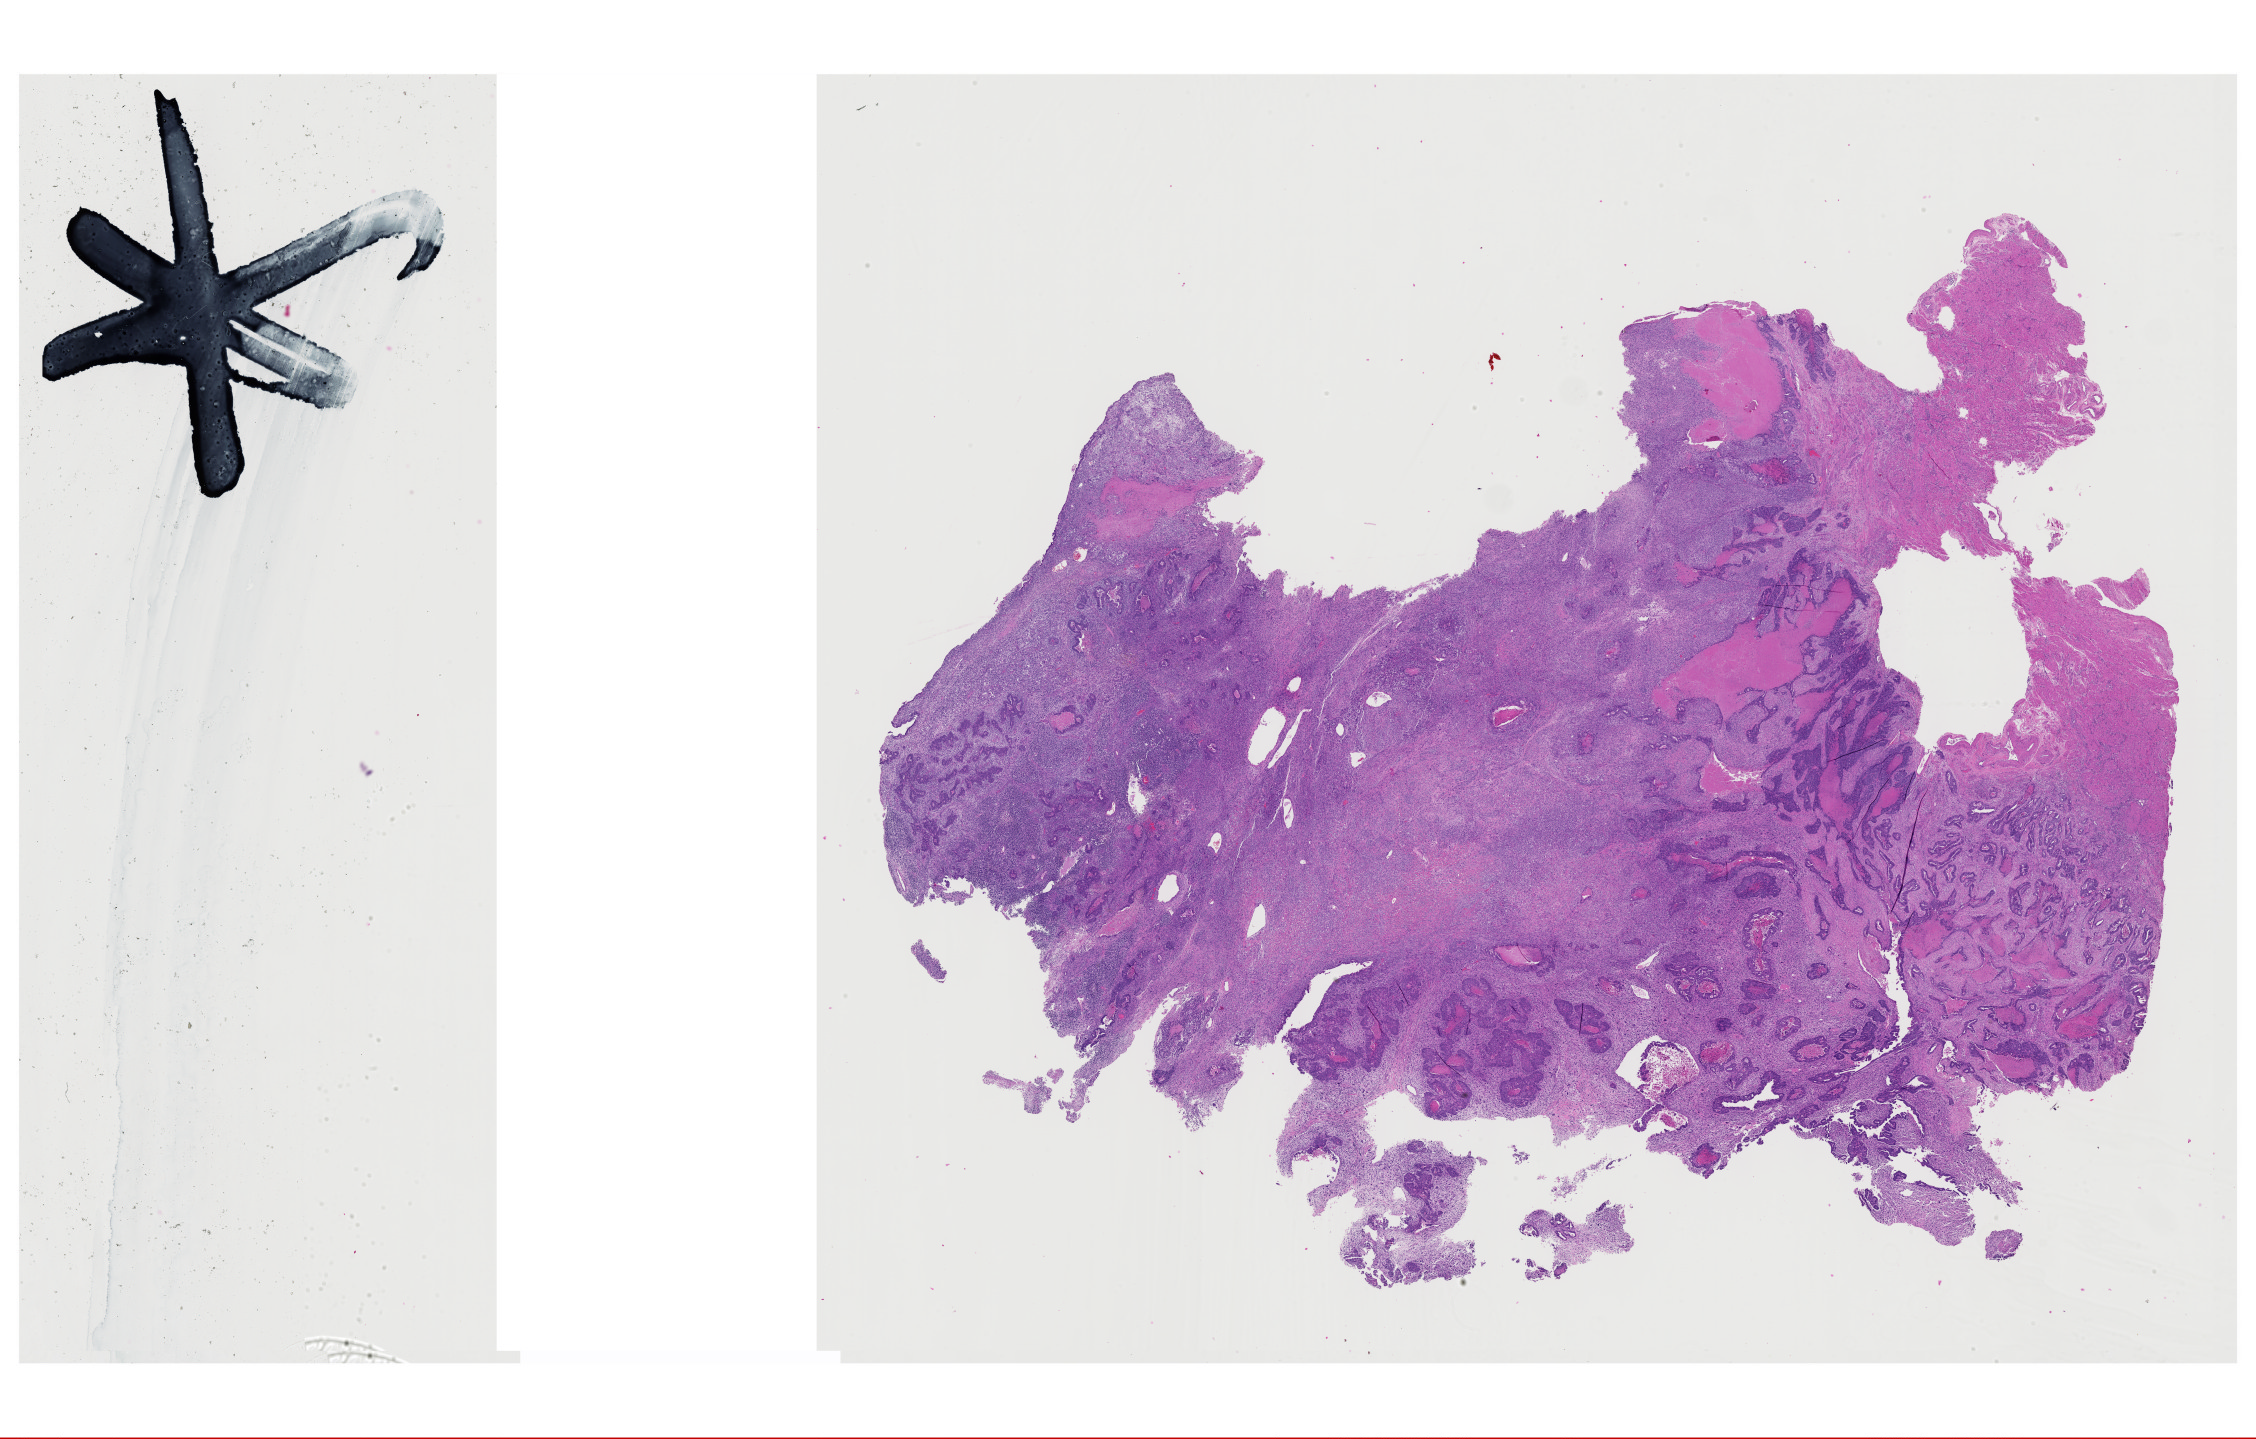
H&E whole-slide image — low-resolution overview of the scanned area, about 36.1 x 23.0 mm; FFPE section; sample: primary tumour, uterus. Patient sex: female.
Histologic diagnosis: Mullerian mixed tumor. Lymph nodes positive (case pathology): 7 of 18 examined. FIGO stage: IIIC2.